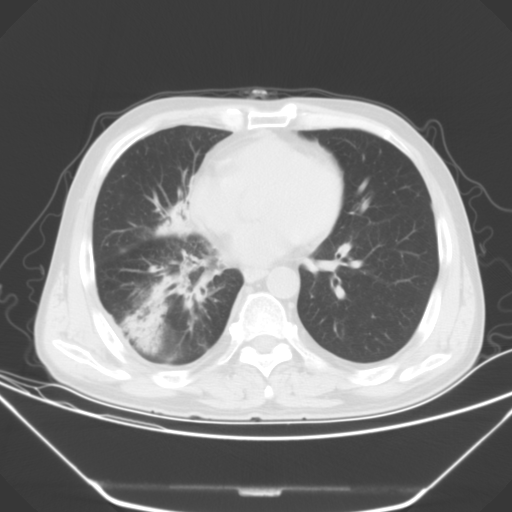
Chest CT, one axial slice. Position 20 of 52 along the scan axis. 120 kVp. Lung window (W 1500 / L -600 HU). 5 mm slice thickness. 512 × 512 image matrix, field of view 379 × 379 mm. Male patient, age 54 years. From the clinical record (not read from this slice): clinical TNM (as recorded): T2 N1 M0.
Structures marked on this image (bounding box drawn by a radiologist):
- lung tumour (recorded histology: adenocarcinoma): bounding box (x1, y1, x2, y2) in pixels: (126, 276, 173, 350)